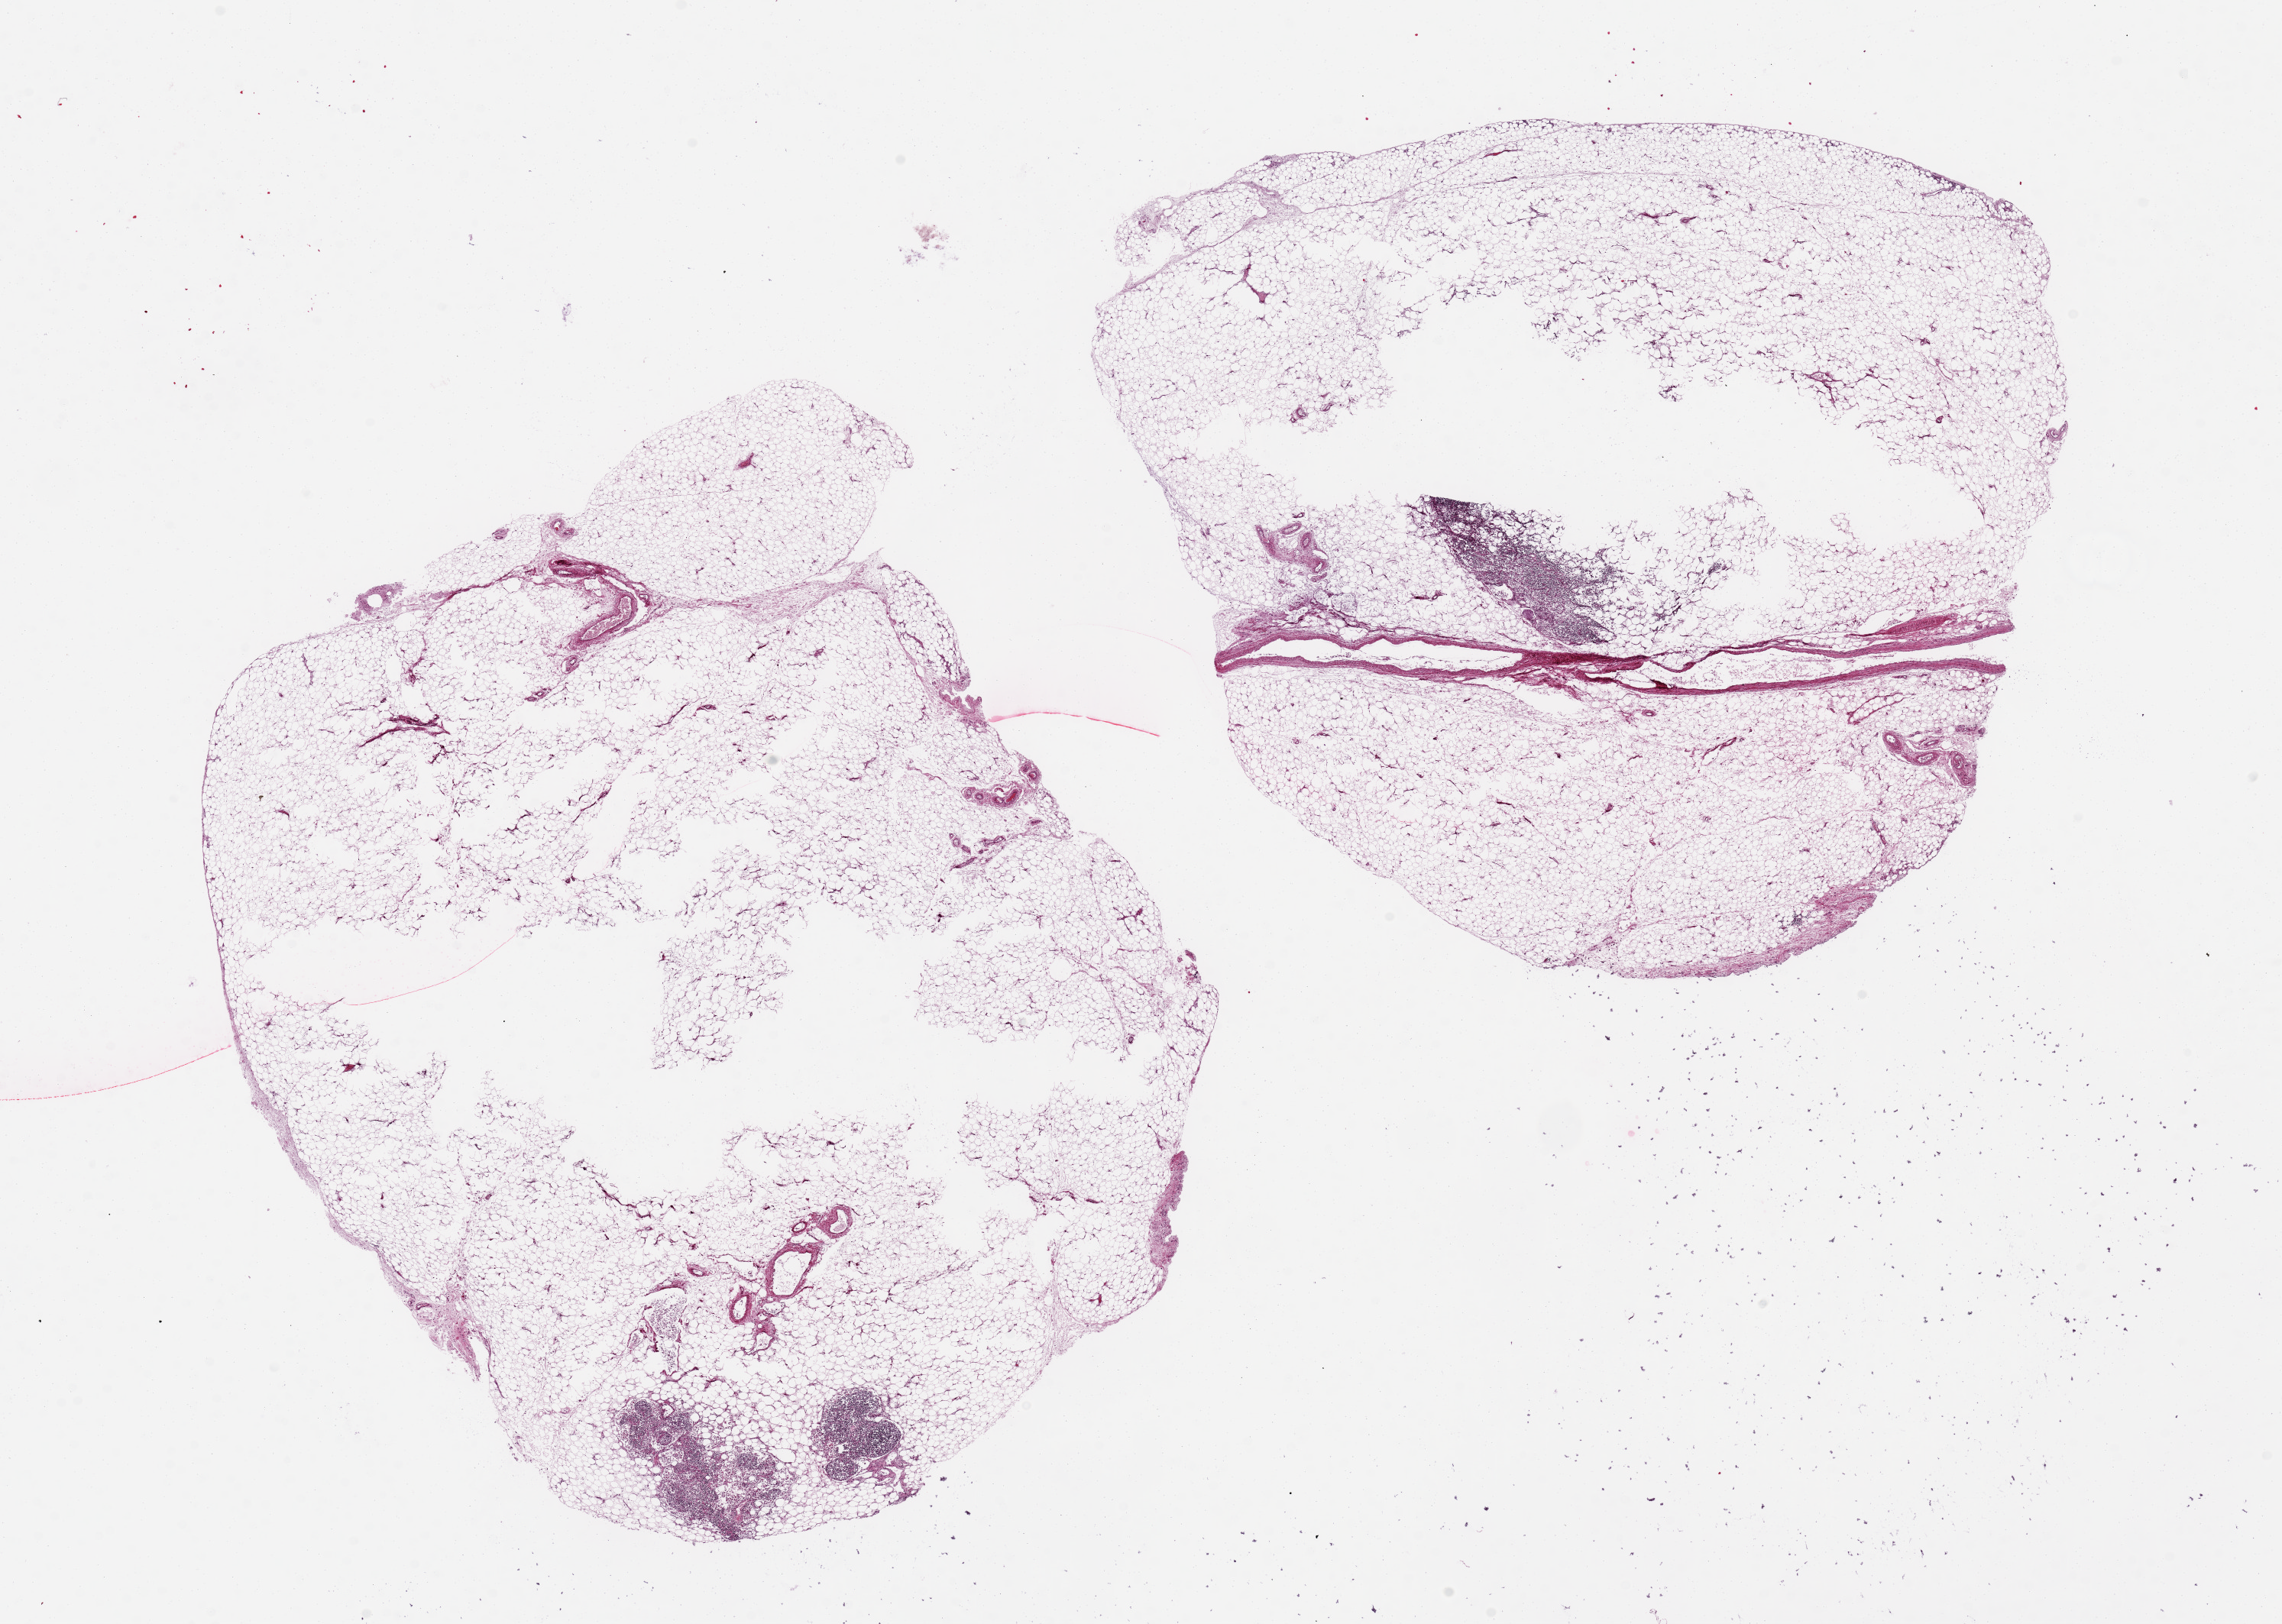
Whole-slide image, haematoxylin and eosin stain — whole scanned area (about 23.6 x 16.8 mm) shown as a low-resolution overview, PAXgene-fixed, paraffin-embedded tissue, sampled site (target tissue): pancreas, tissue donor sample. Donor sex: female.
Review note (as recorded): 2 pieces 10x8&9x9 mm; 100% adipose tissue with focal lymphoid aggregates; no pancreas present.